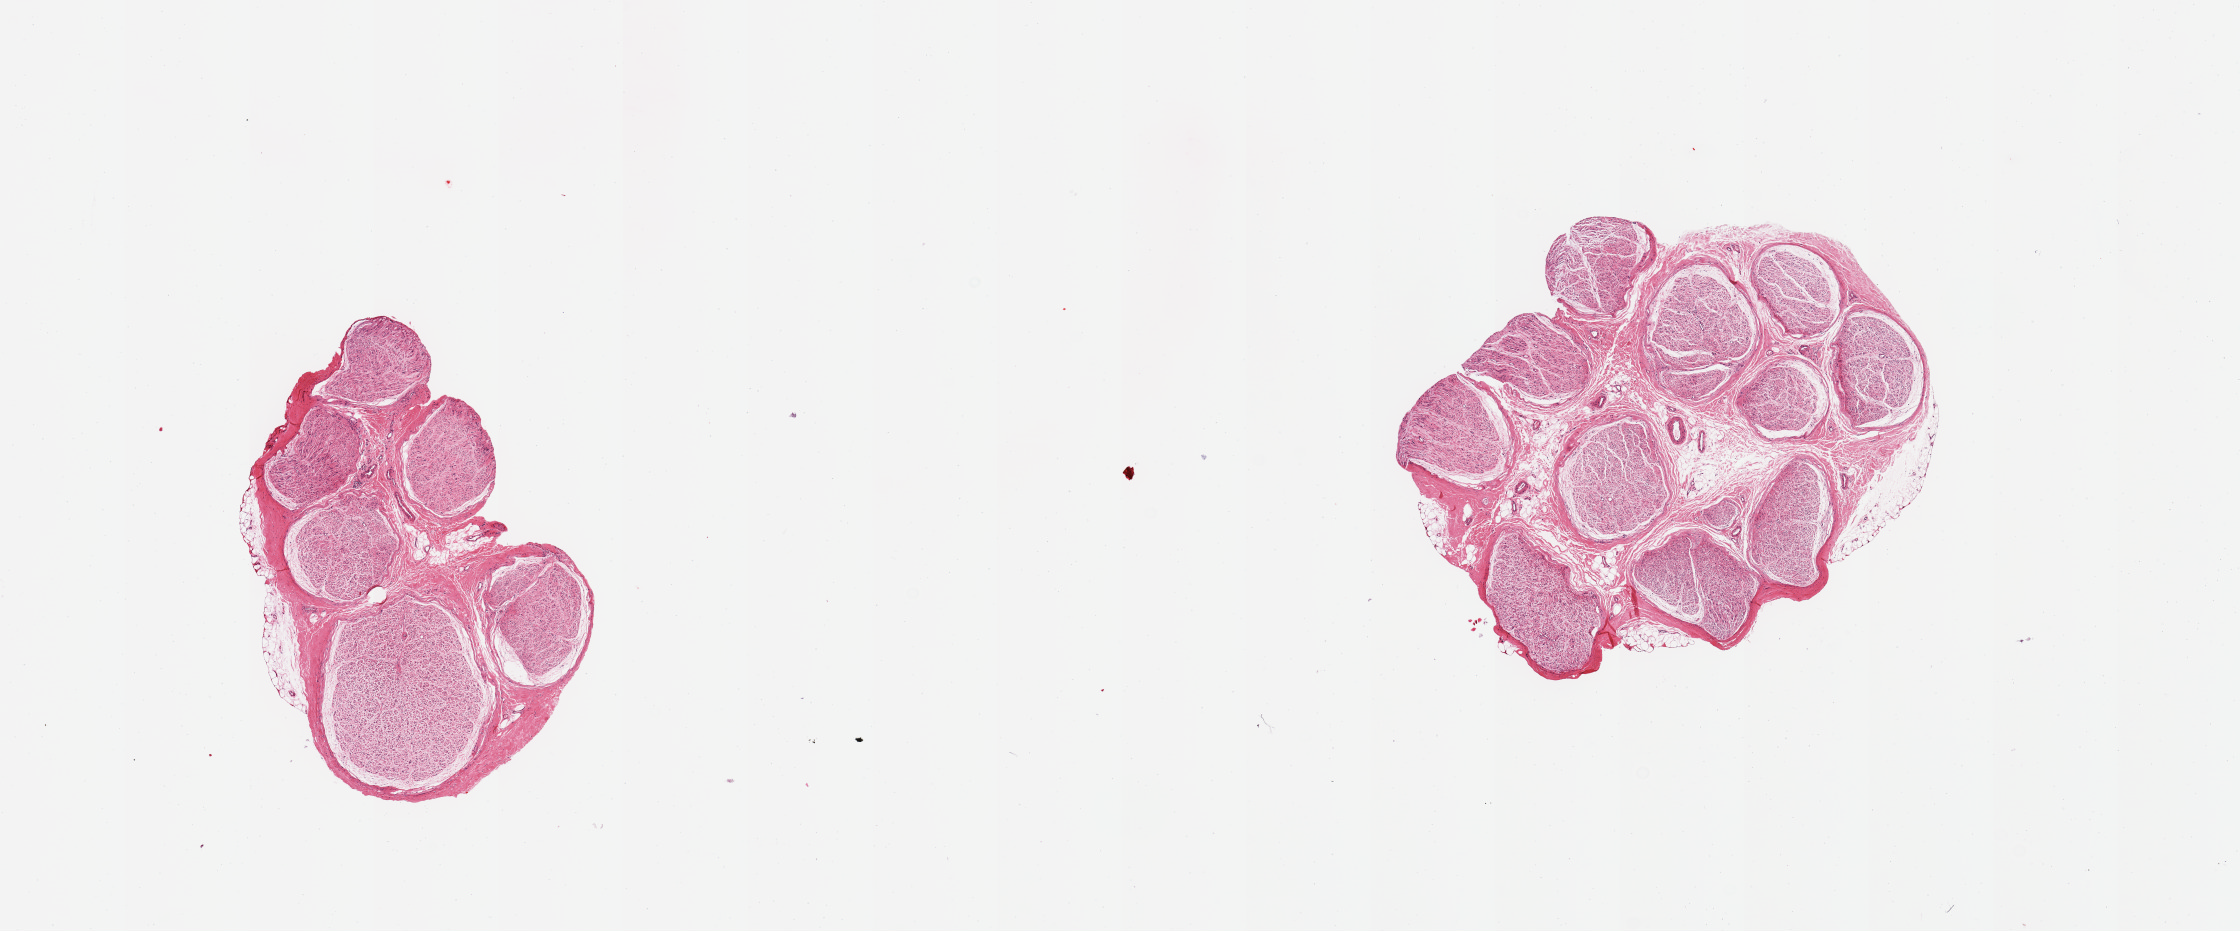
Whole-slide image, haematoxylin and eosin stain — a low-resolution overview of the entire scanned area, about 17.7 x 7.4 mm (slide scanned at 20x). PAXgene-fixed paraffin-embedded (PFPE) section. Target tissue: tibial nerve. Tissue donor sample. Male donor.
- review note (as recorded): 2 pieces; essentially well trimmed